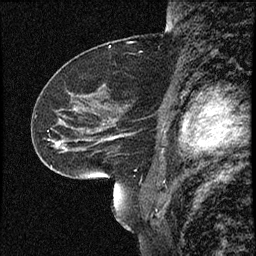
Breast MRI (dynamic contrast-enhanced), one sagittal slice; position 35 of 60 along the scan axis; dynamic contrast-enhanced study with each time point stored as its own series, time point 2 of 4 at this slice position (early post-contrast, ordered by acquisition time); 1.5 T; TE 4.2 ms, TR 16.7 ms; 256 × 256 image matrix, field of view 200 × 200 mm. Patient: female, 52 years. Case-level facts recorded for this patient, not image findings: setting: breast cancer imaged before/during neoadjuvant chemotherapy; receptor status: HER2-positive.
Structures marked on this image (semi-automatically segmented with operator editing):
- analysis volume of interest (the breast-tissue region the enhancement analysis was run in; not a lesion): bounding box <37,79,165,181> (left, top, right, bottom; pixels)
- tumour enhancement mask (voxels above the 100 % enhancement threshold inside the analysis volume of interest): <58,136,117,144>